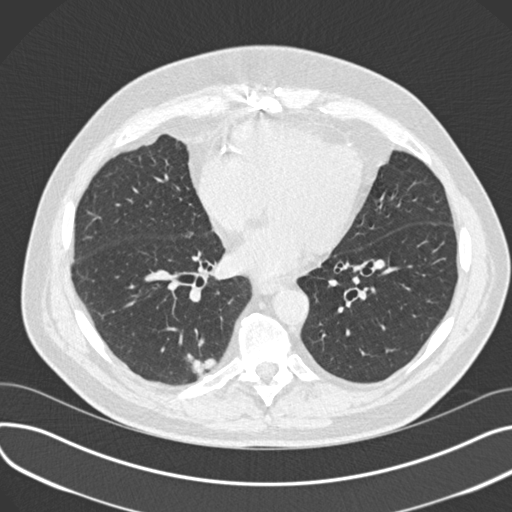
Low-dose screening chest CT, one axial slice. Slice 74 of 177 in the series (ordered by position). Lung window (W 1500 / L -600 HU). 2 mm slice thickness. 512 × 512 image matrix, field of view 372 × 372 mm.
Outlined on this slice (expert manual segmentation):
- lesion 1 (tumor, lower lobe of right lung): bounding box (x1, y1, x2, y2) in pixels: (186, 354, 216, 378)